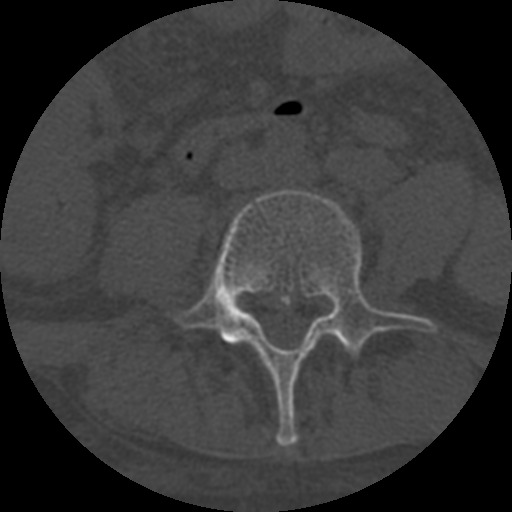
CT including the spine, one axial slice. Slice 209 of 708 in the series (ordered by position). One of 3 acquisitions stored at this slice position. Bone window (W 1800 / L 400 HU). 1.25 mm slice thickness. 512 × 512 image matrix, field of view 160 × 160 mm. Patient age 55 years. Case-level facts recorded for this patient, not image findings: primary cancer: colon; vertebrae with lytic lesions (as recorded): T12, L1, L5.
Structures marked on this image (semi-automatic segmentation, software-assisted and operator-edited):
- L4 vertebra: bounding box [x1, y1, x2, y2] px = [175, 189, 436, 447]